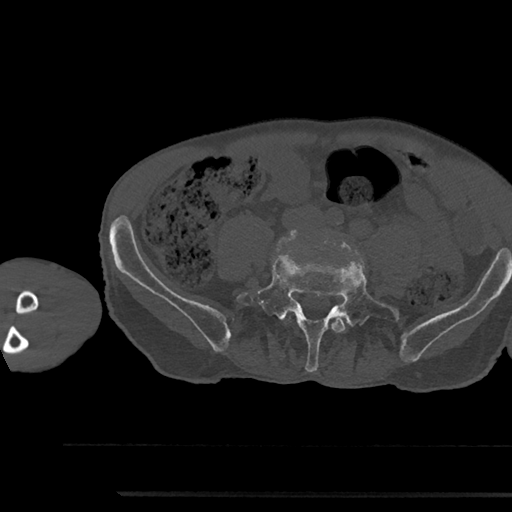
CT including the spine, one axial slice; slice 361 of 797 in the series (ordered by position); reconstruction kernel Br40s/3; bone window (W 1800 / L 400 HU); 0.5 mm slice thickness; 512 × 512 image matrix, field of view 367 × 367 mm. Male patient, age 79 years. From the clinical record (not read from this slice): primary cancer: prostate.
Annotated regions visible in this slice (semi-automatic segmentation, software-assisted and operator-edited):
- L4 vertebra: bounding box <332,318,345,333> (left, top, right, bottom; pixels)
- L5 vertebra: <236,255,401,372>